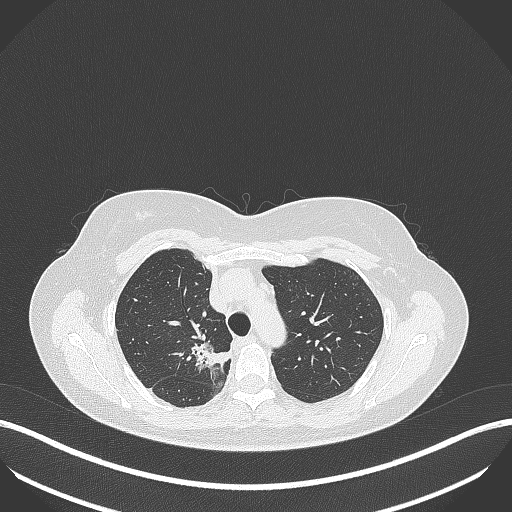
Chest CT, one axial slice. Slice 296 of 386 in the series (ordered by position). Reconstruction kernel B70f. Lung window (W 1500 / L -600 HU). 1 mm slice thickness. 512 × 512 image matrix. Female patient, age 65 years. Case-level facts recorded for this patient, not image findings: clinical TNM (as recorded): T1b N0 M0.
Outlined on this slice (bounding box drawn by a radiologist):
- lung tumour (recorded histology: adenocarcinoma): bounding box [x1, y1, x2, y2] px = [190, 334, 233, 375]